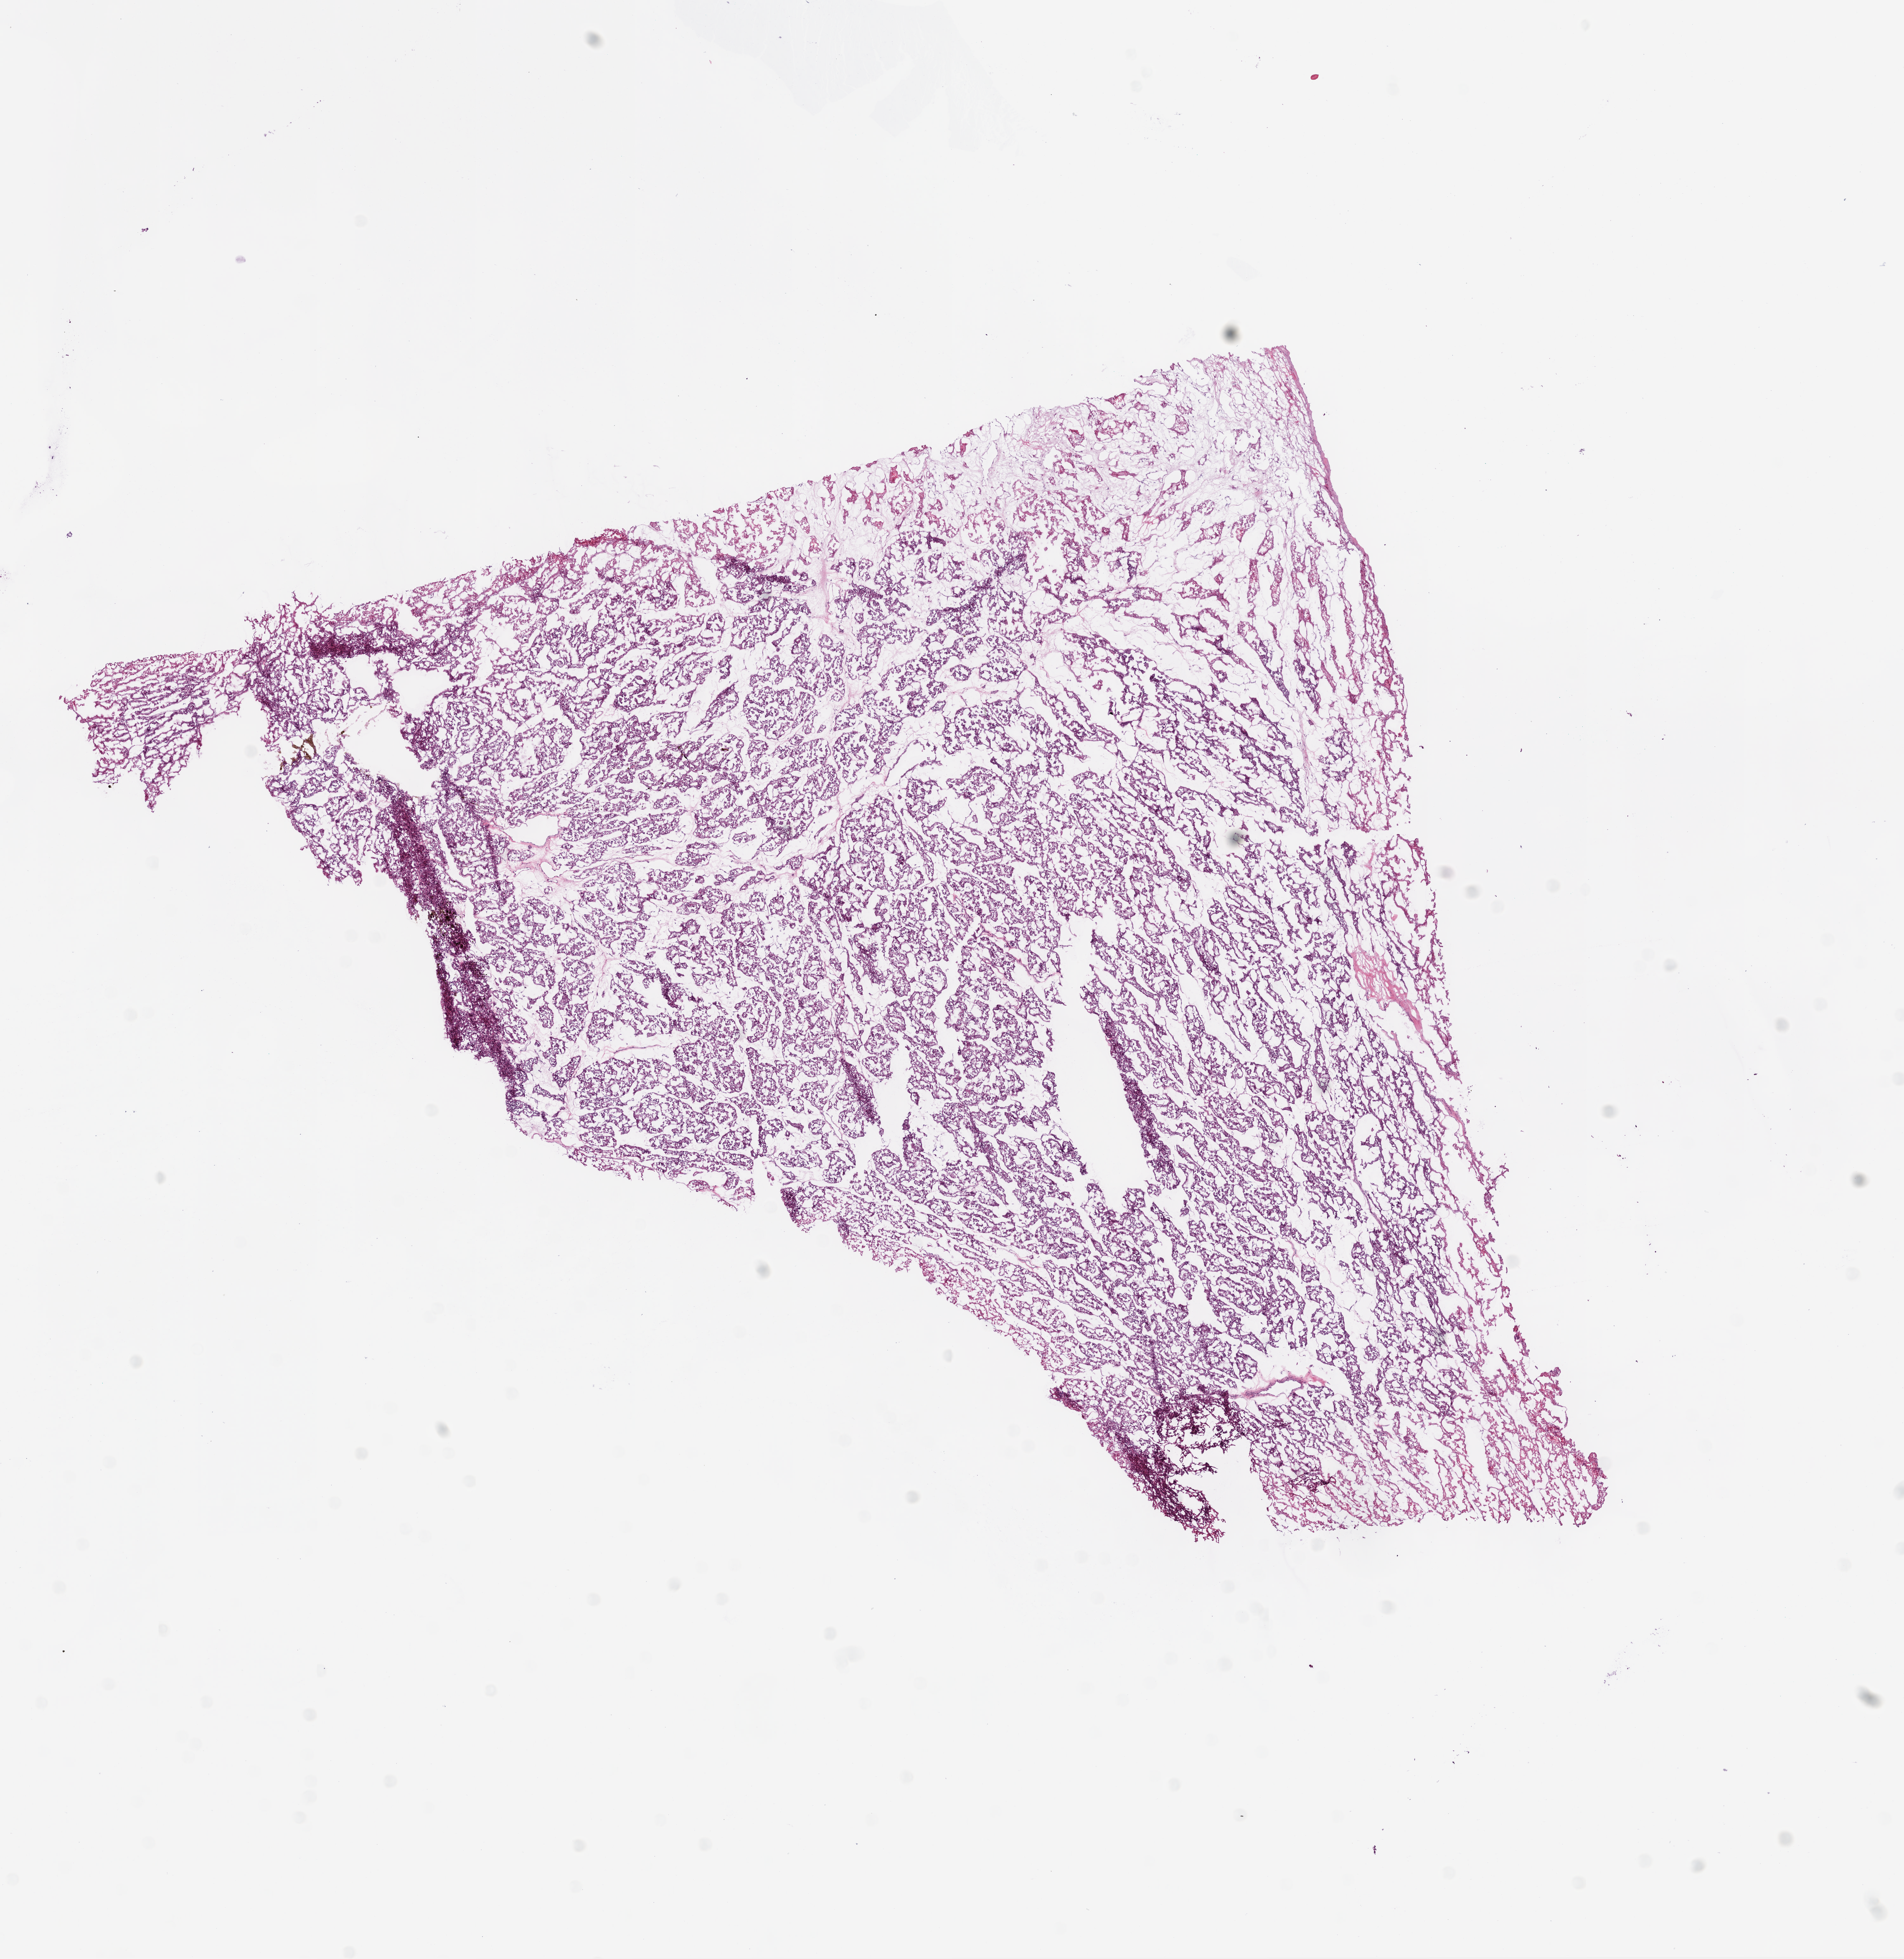
H&E whole-slide image, whole scanned area (about 12.0 x 12.4 mm, from a 20x scan) shown as a low-resolution overview, frozen section, kidney, primary tumour sample. Male patient; age at initial diagnosis 45 years. Slide review estimates, as recorded: tumour cells 90%, tumour nuclei 85%.
Histologic diagnosis: Clear cell adenocarcinoma, NOS.